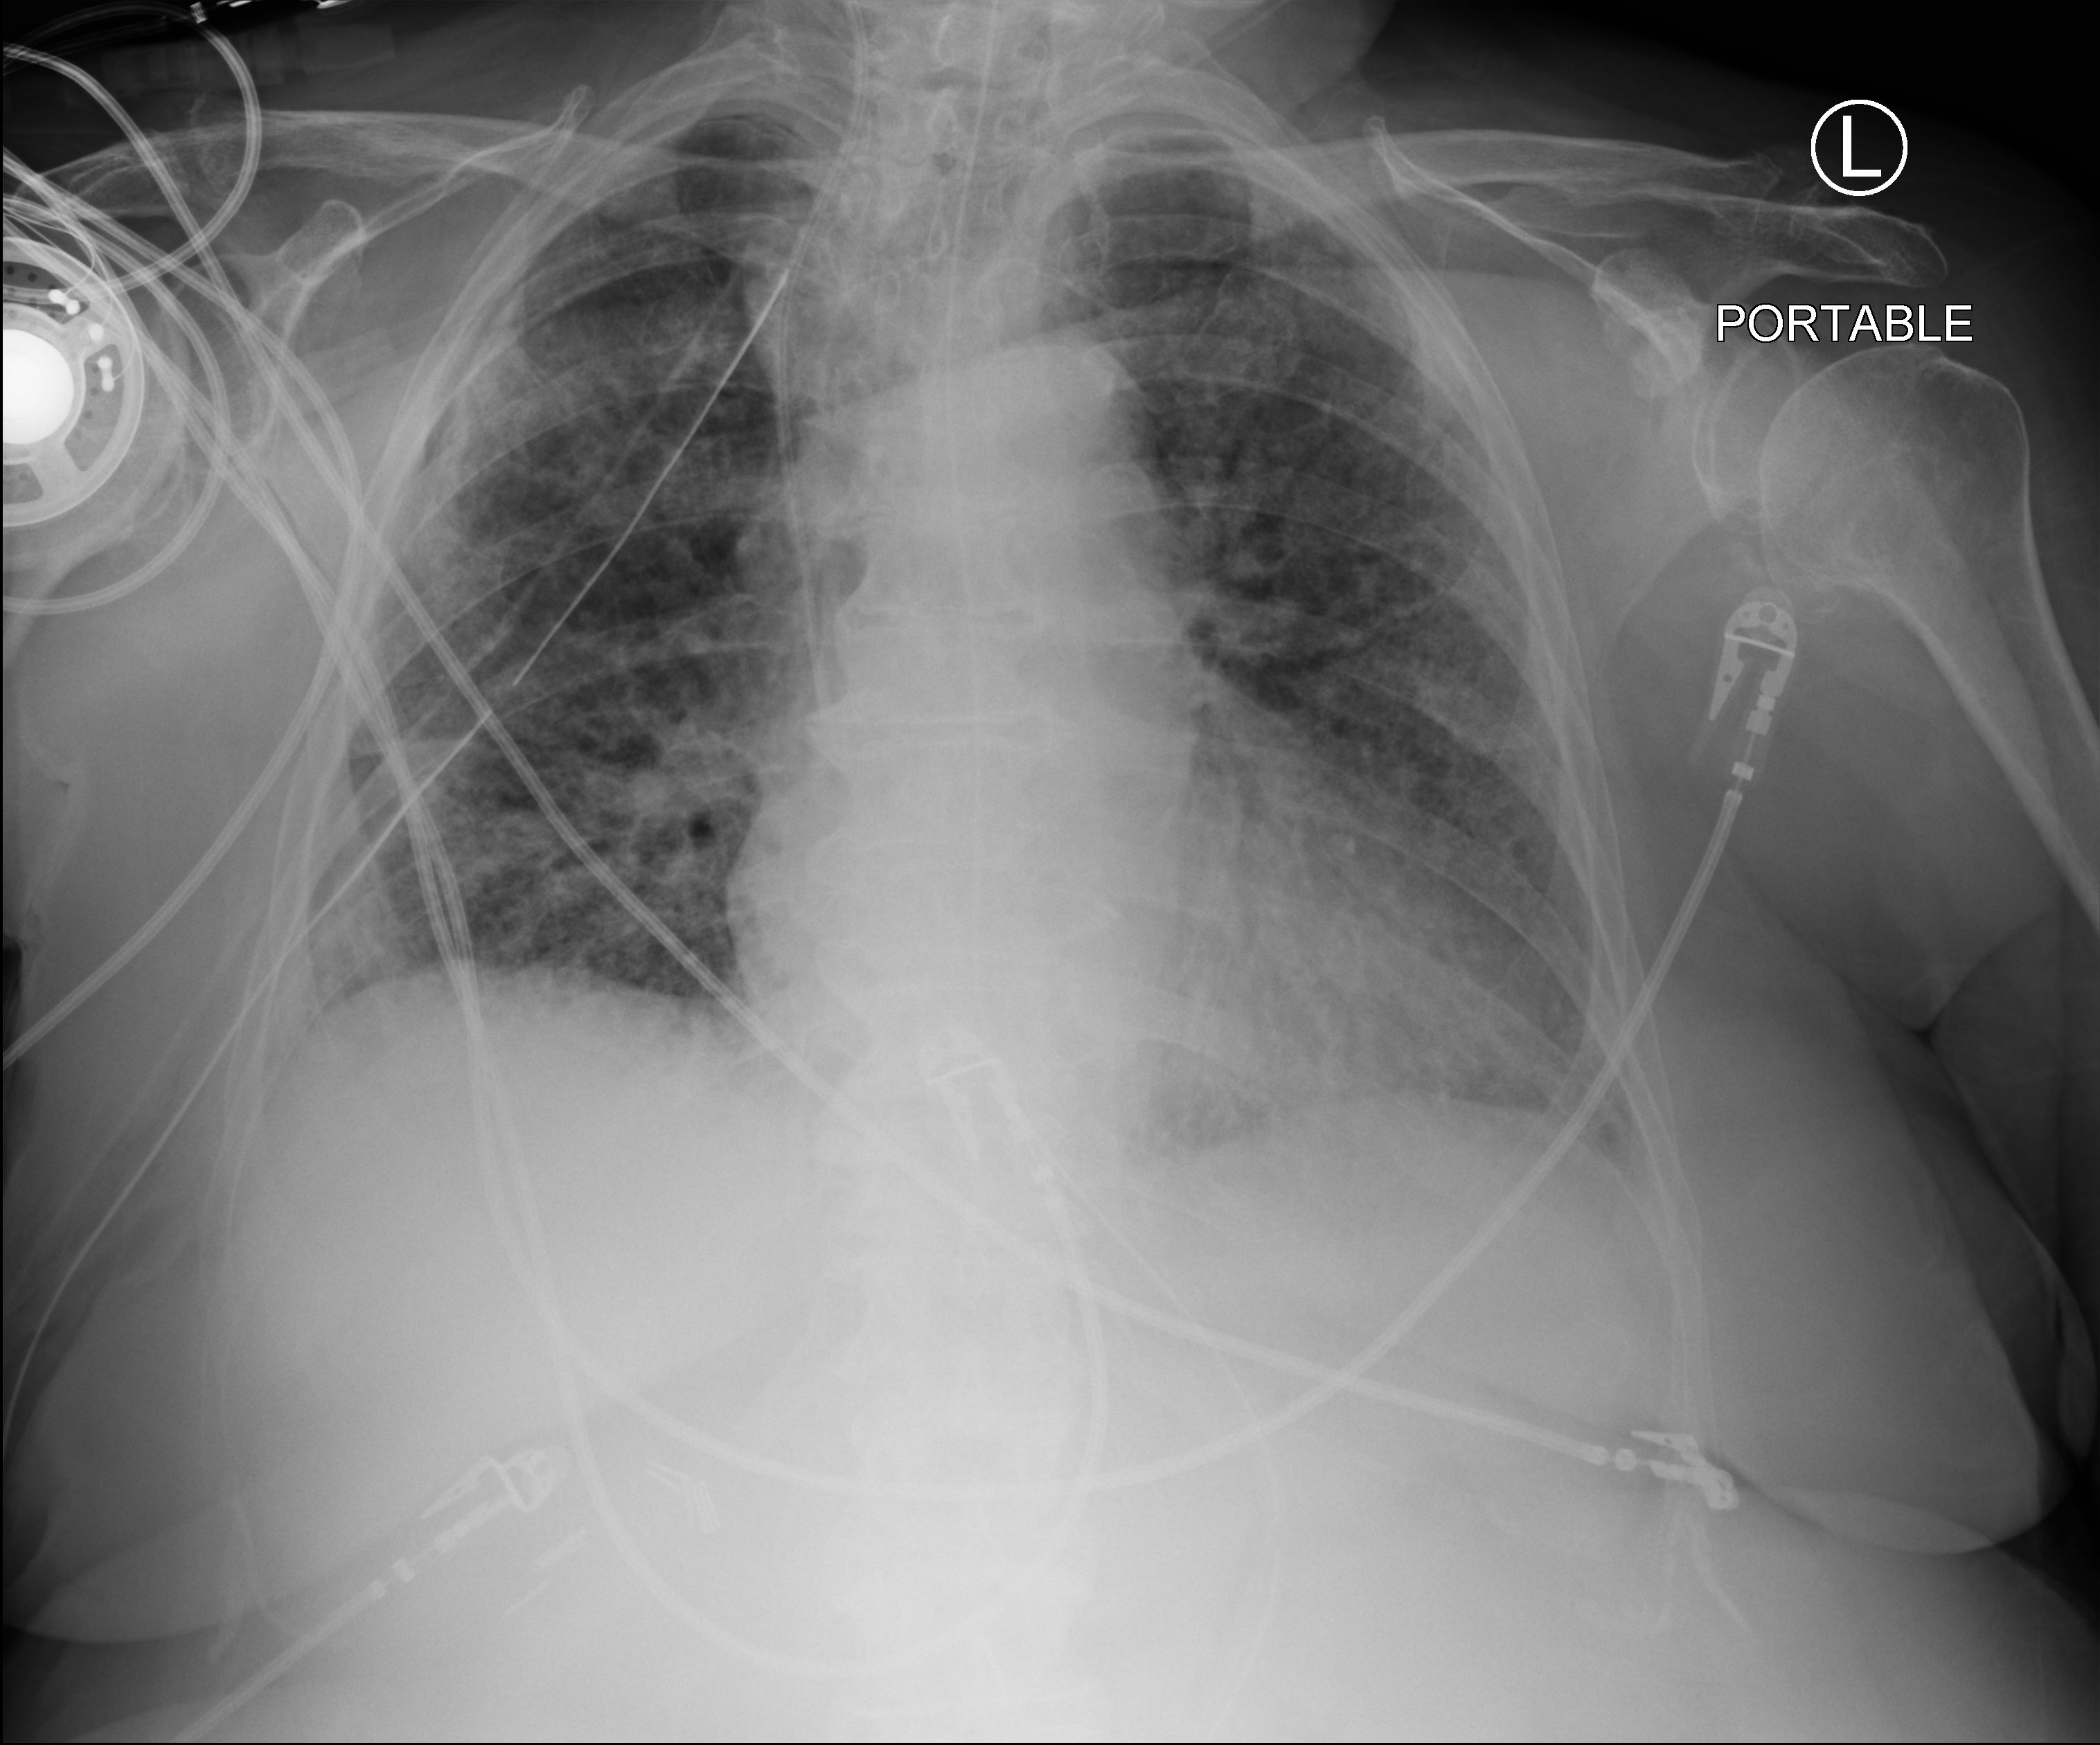
Portable chest radiograph. Female patient hospitalised with COVID-19, age 75–90 years.
Hospital-stay facts (about this admission, not read from this image; timing relative to this image not recorded):
- mechanically ventilated during this hospital stay: yes